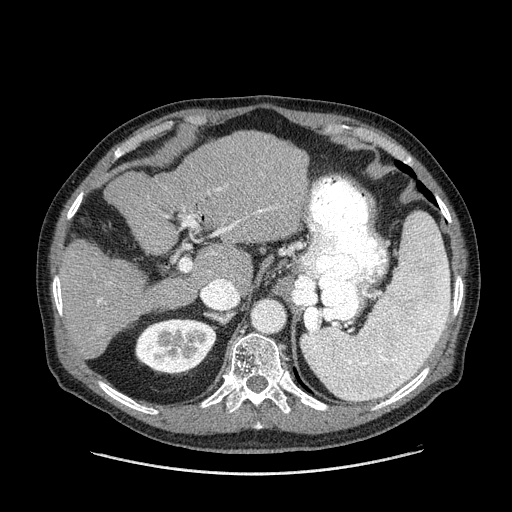
Contrast-enhanced abdominal CT (liver protocol), one axial slice; position 92 of 180 along the scan axis; reconstruction kernel STANDARD; one of 2 acquisitions stored at this slice position; soft-tissue window (W 400 / L 40 HU); 2.5 mm slice thickness; 512 × 512 image matrix, field of view 420 × 420 mm. Case-level facts recorded for this patient, not image findings: diagnosis: hepatocellular carcinoma (patient treated with transarterial chemoembolisation; whether this scan precedes or follows treatment is not stated here); TNM stage (as recorded): Stage-II.
Structures marked on this image (semi-automatically segmented with operator editing):
- liver parenchyma outside the tumour (the mass and vessels are separate outlines, so this box may not span the whole liver): box from (x=58, y=132) to (x=308, y=358) px
- liver vessels: (x=98, y=187)–(x=272, y=303)